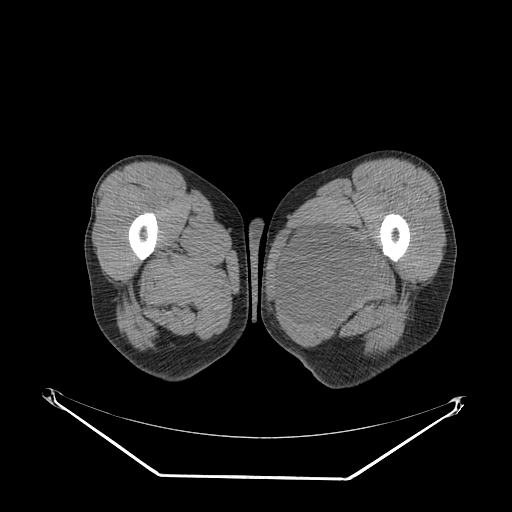
CT of an extremity soft-tissue mass (from a PET/CT study), one axial slice. Slice 30 of 267 in the series (ordered by position). Reconstruction kernel SOFT. 140 kVp. Soft-tissue window (W 400 / L 40 HU). 512 × 512 image matrix, field of view 500 × 500 mm. Male patient. Case-level facts recorded for this patient, not image findings: histological type: pleiomorphic liposarcoma; grade: high; site of the primary tumour: left thigh.
Structures marked on this image (expert contour drawn on MRI and transferred to this co-registered scan by the dataset authors):
- gross tumour volume including surrounding oedema: bounding box (x1, y1, x2, y2) in pixels: (283, 222, 382, 321)
- gross tumour volume (mass): (285, 226, 378, 314)